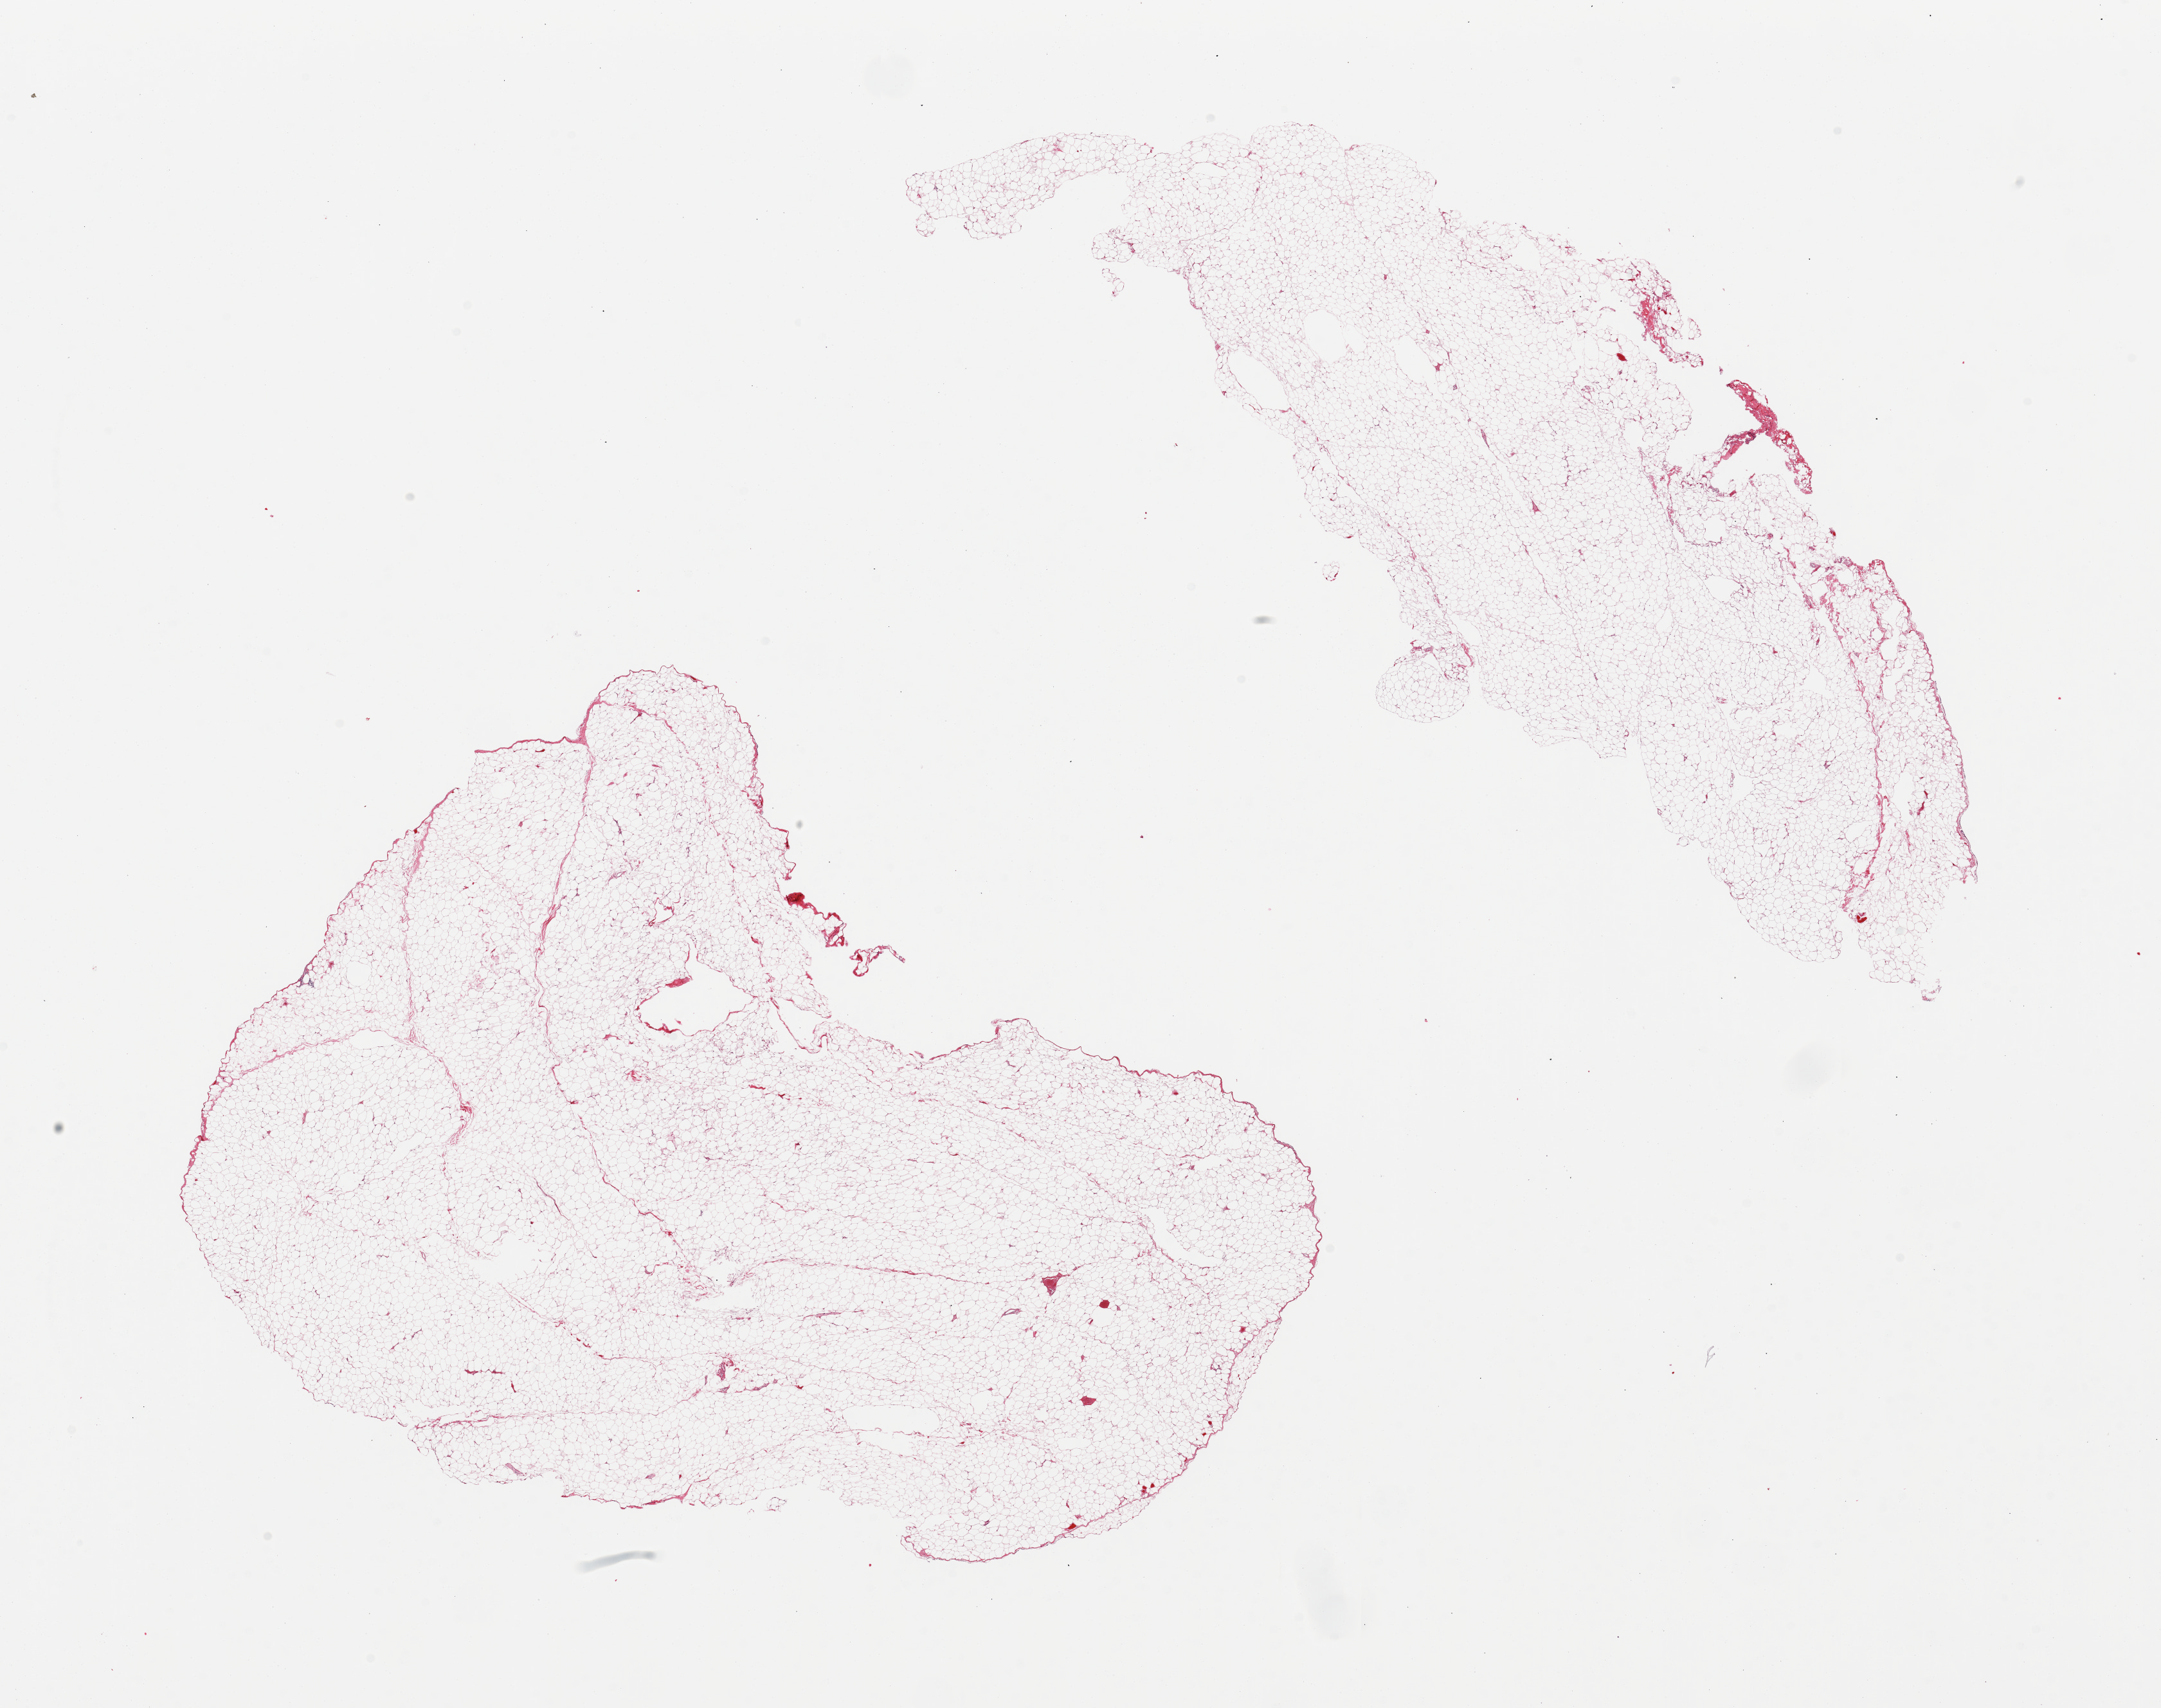
H&E whole-slide image, brightfield, whole scanned area (about 26.6 x 21.0 mm) shown as a low-resolution overview, PAXgene-fixed, paraffin-embedded tissue, target tissue: omentum, donor tissue sample. Donor: male.
Reviewer comment on this tissue sample: 2 pieces.